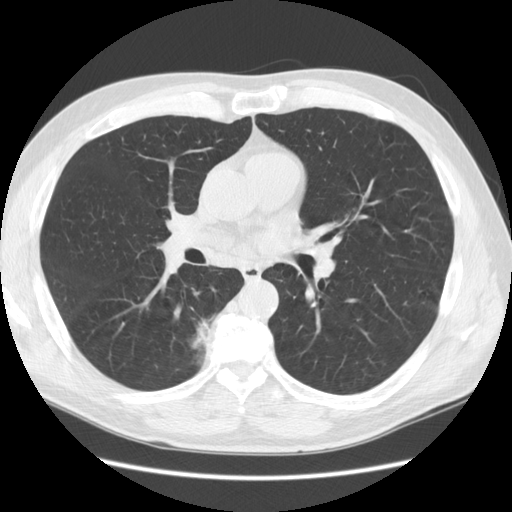
Low-dose screening chest CT, one axial slice. Slice 72 of 133 in the series (ordered by position). Reconstruction kernel STANDARD. 120 kVp. Lung window (W 1500 / L -600 HU). 512 × 512 image matrix, field of view 370 × 370 mm.
Outlined on this slice (outlined manually by an expert reader):
- lesion 1 (tumor, lower lobe of right lung): bounding box (x1, y1, x2, y2) in pixels: (195, 316, 215, 348)